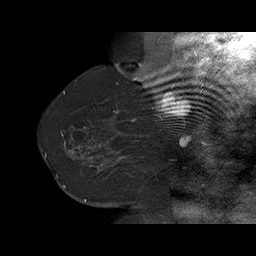
Breast MRI (dynamic contrast-enhanced), one sagittal slice. Slice 52 of 75 in the series (ordered by position). Dynamic contrast-enhanced series, time point 2 of 6 at this slice position (early post-contrast). 1.5 T. TE 4.5 ms, TR 32.4 ms. 3 mm slice thickness. 256 × 256 image matrix, field of view 180 × 180 mm. Female patient. Case-level facts recorded for this patient, not image findings: setting: breast cancer imaged before/during neoadjuvant chemotherapy; receptor status: HR-positive, HER2-negative.
Outlined on this slice (semi-automatic segmentation, software-assisted and operator-edited):
- analysis volume of interest (the breast-tissue region the enhancement analysis was run in; not a lesion): bounding box [x1, y1, x2, y2] px = [58, 134, 166, 191]
- tumour enhancement mask (voxels above the 100 % enhancement threshold inside the analysis volume of interest): [61, 134, 124, 187]